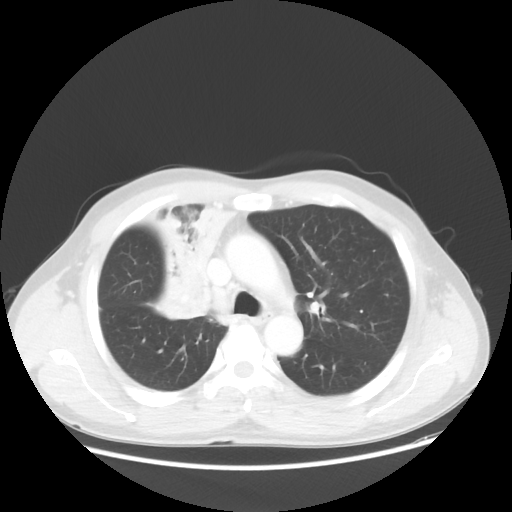
Chest CT, one axial slice; slice 37 of 56 in the series (ordered by position); reconstruction kernel STANDARD; lung window (W 1500 / L -600 HU); 5 mm slice thickness; 512 × 512 image matrix, field of view 398 × 398 mm. Male patient, age 60 years. From the clinical record (not read from this slice): clinical TNM (as recorded): T2a N1 M0.
Structures marked on this image (rectangle marked by the reading radiologist):
- lung tumour (recorded histology: squamous cell carcinoma): bounding box <122,192,239,324> (left, top, right, bottom; pixels)